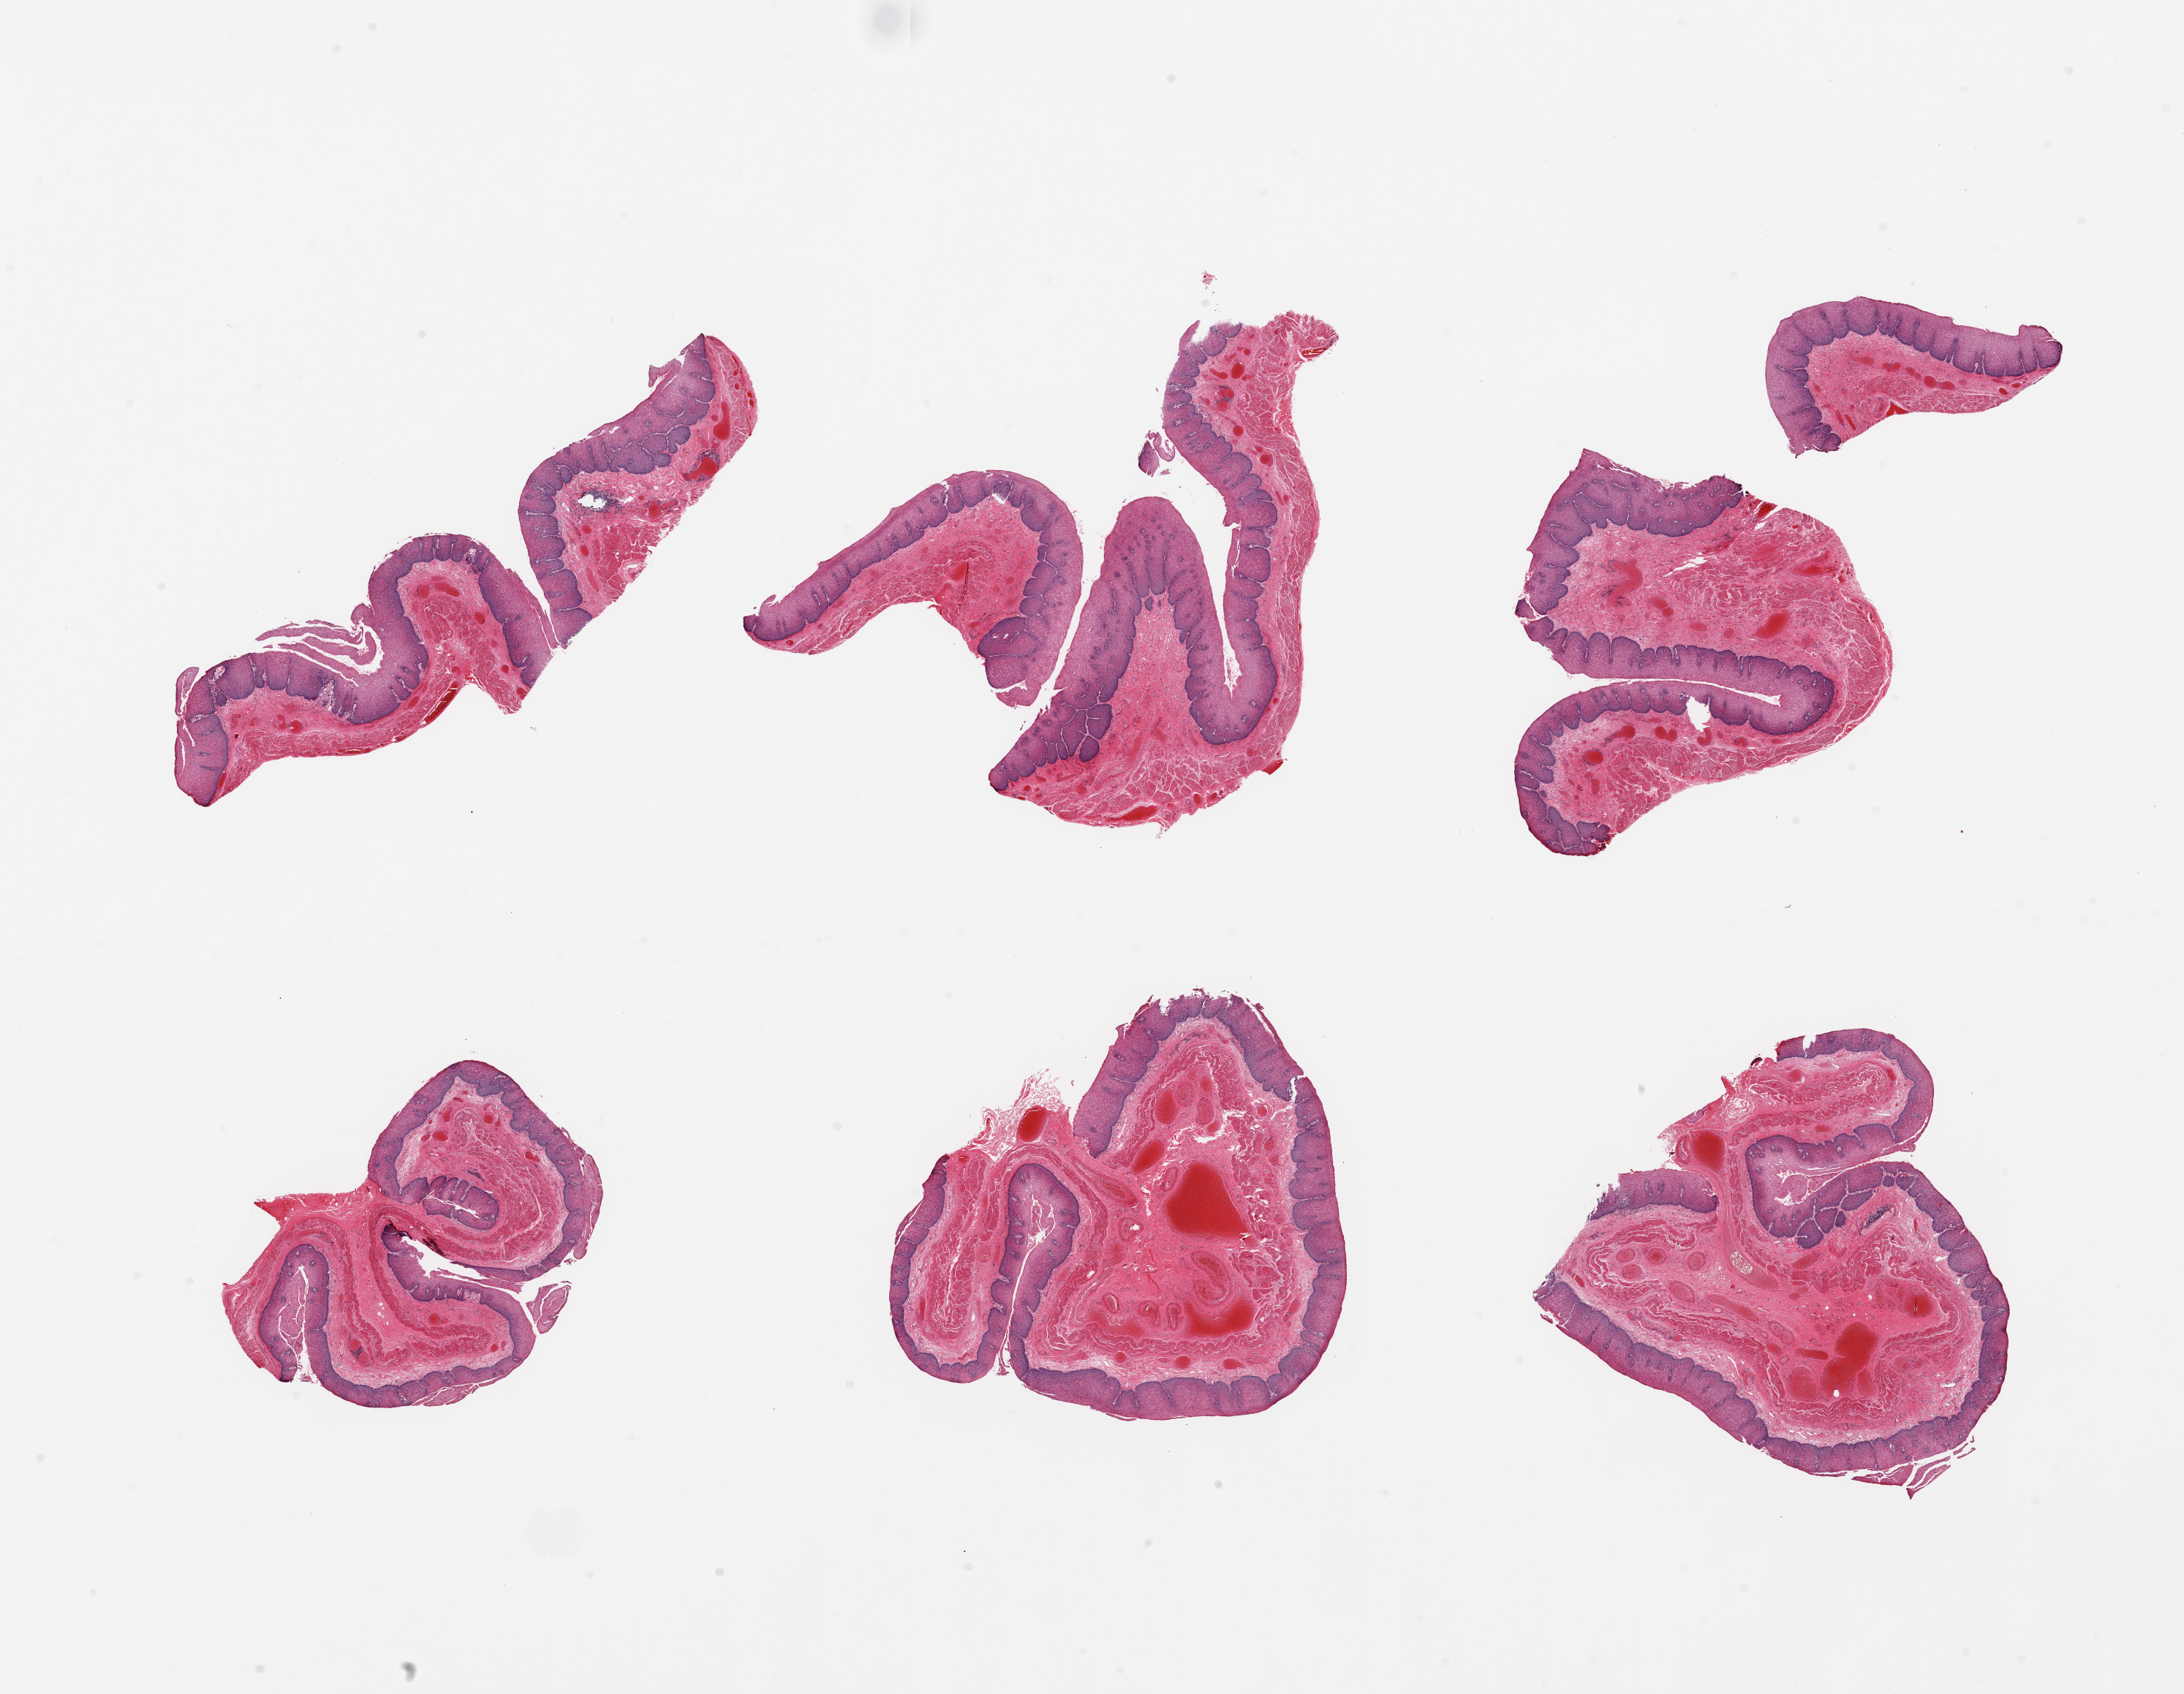
Digitized hematoxylin and eosin (H&E)-stained section — whole scanned area (about 23.6 x 18.3 mm) shown as a low-resolution overview, PAXgene-fixed, paraffin-embedded tissue, target tissue: esophageal mucous membrane, donor tissue sample. Male donor.
Reviewer comment on this tissue sample: 6 pieces, squamous mucosa is ~0.5mm, ~20% thickness.